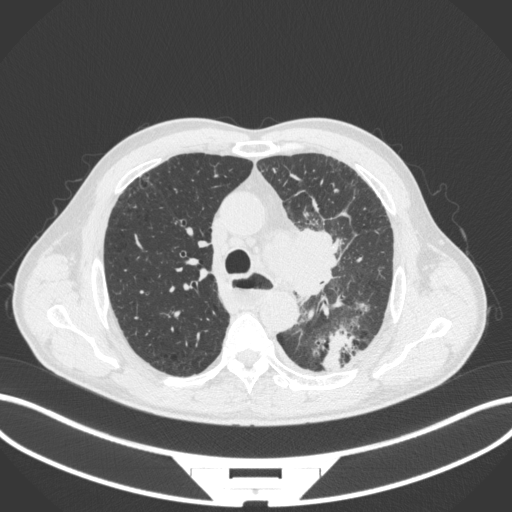
Chest CT, one axial slice. Slice 266 of 411 in the series (ordered by position). Lung window (W 1500 / L -600 HU). 1 mm slice thickness. 512 × 512 image matrix, field of view 400 × 400 mm. Male patient, age 57 years. Case-level facts recorded for this patient, not image findings: clinical TNM (as recorded): T2a N1 M0.
Outlined on this slice (bounding box drawn by a radiologist):
- lung tumour (recorded histology: squamous cell carcinoma): bounding box (x1, y1, x2, y2) in pixels: (262, 221, 352, 302)